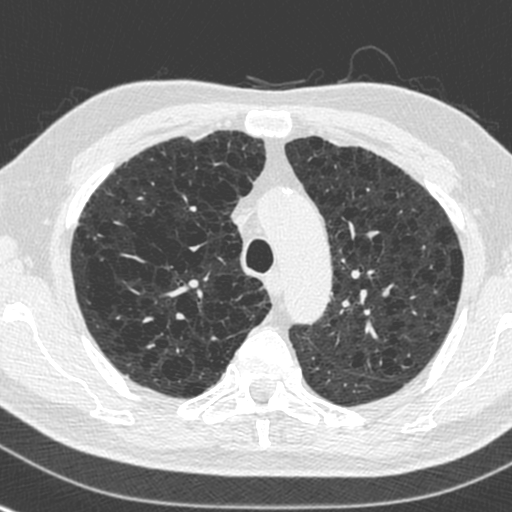
Low-dose screening chest CT, axial slice; first (baseline) screen; lung window (W 1500 / L -600 HU); 1.3 mm slice thickness; slice 63 of 250 in the series. Male participant, aged 73 years at enrolment.
Expert-annotated lung lesion, box from (x=152, y=249) to (x=198, y=286) px. Screening reader's record for this exam: no non-calcified nodule ≥4 mm recorded. Later outcome: lung cancer diagnosed 446 days after this screen (after the second annual screen) — squamous cell carcinoma, NOS, right upper lobe, stage IA (AJCC 6th edition), 10 mm at pathology.